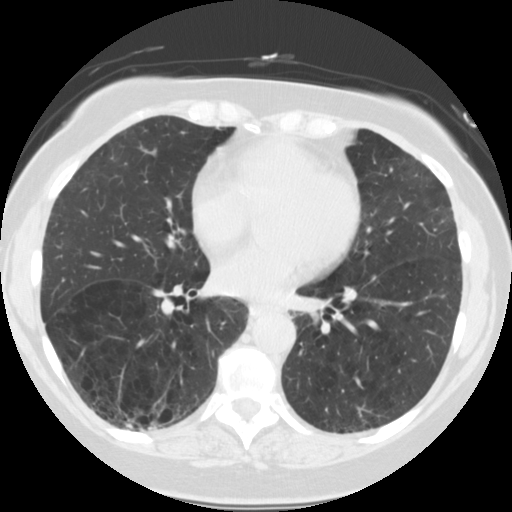
Axial slice from a low-dose chest CT screening exam; first (baseline) screen; lung window (W 1500 / L -600 HU); slice 75 of 121 in the series; 512 × 512 image matrix, field of view 309 × 309 mm. Female participant, aged 59 years at enrolment. Current smoker at enrolment.
Lesion marked by an expert reader, bounding box [x1, y1, x2, y2] px = [104, 397, 158, 445]. Screening reader's record for this exam: no non-calcified nodule ≥4 mm recorded. Official screen result: negative screen, significant abnormalities not suspicious for lung cancer. Later outcome: lung cancer diagnosed 443 days after this screen — squamous cell carcinoma, NOS, right lower lobe, poorly differentiated (G3), stage IB (AJCC 6th edition), 30 mm at pathology.